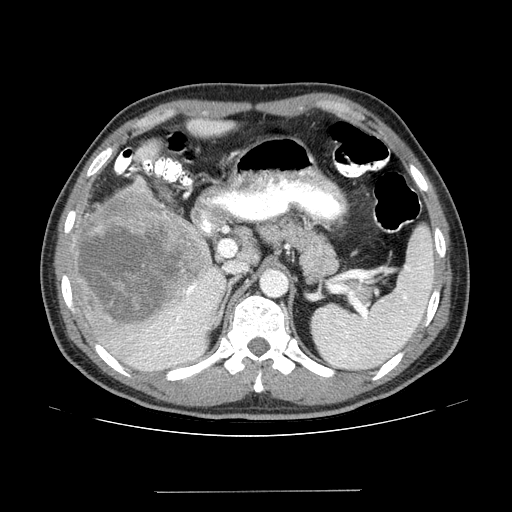
Contrast-enhanced abdominal CT (liver protocol), one axial slice. Position 86 of 131 along the scan axis. Reconstruction kernel STANDARD. 100 kVp. One of 2 acquisitions stored at this slice position. Soft-tissue window (W 400 / L 40 HU). 2.5 mm slice thickness. 512 × 512 image matrix, field of view 380 × 380 mm. Case-level facts recorded for this patient, not image findings: diagnosis: hepatocellular carcinoma (patient treated with transarterial chemoembolisation; whether this scan precedes or follows treatment is not stated here); TNM stage (as recorded): Stage-I; Child-Pugh class: A; tumour size: 10.3 cm.
Outlined on this slice (semi-automatic segmentation, software-assisted and operator-edited):
- liver parenchyma outside the tumour (the mass and vessels are separate outlines, so this box may not span the whole liver): bounding box [x1, y1, x2, y2] px = [68, 176, 226, 372]
- mass: [67, 187, 210, 327]
- liver vessels: [139, 286, 223, 358]